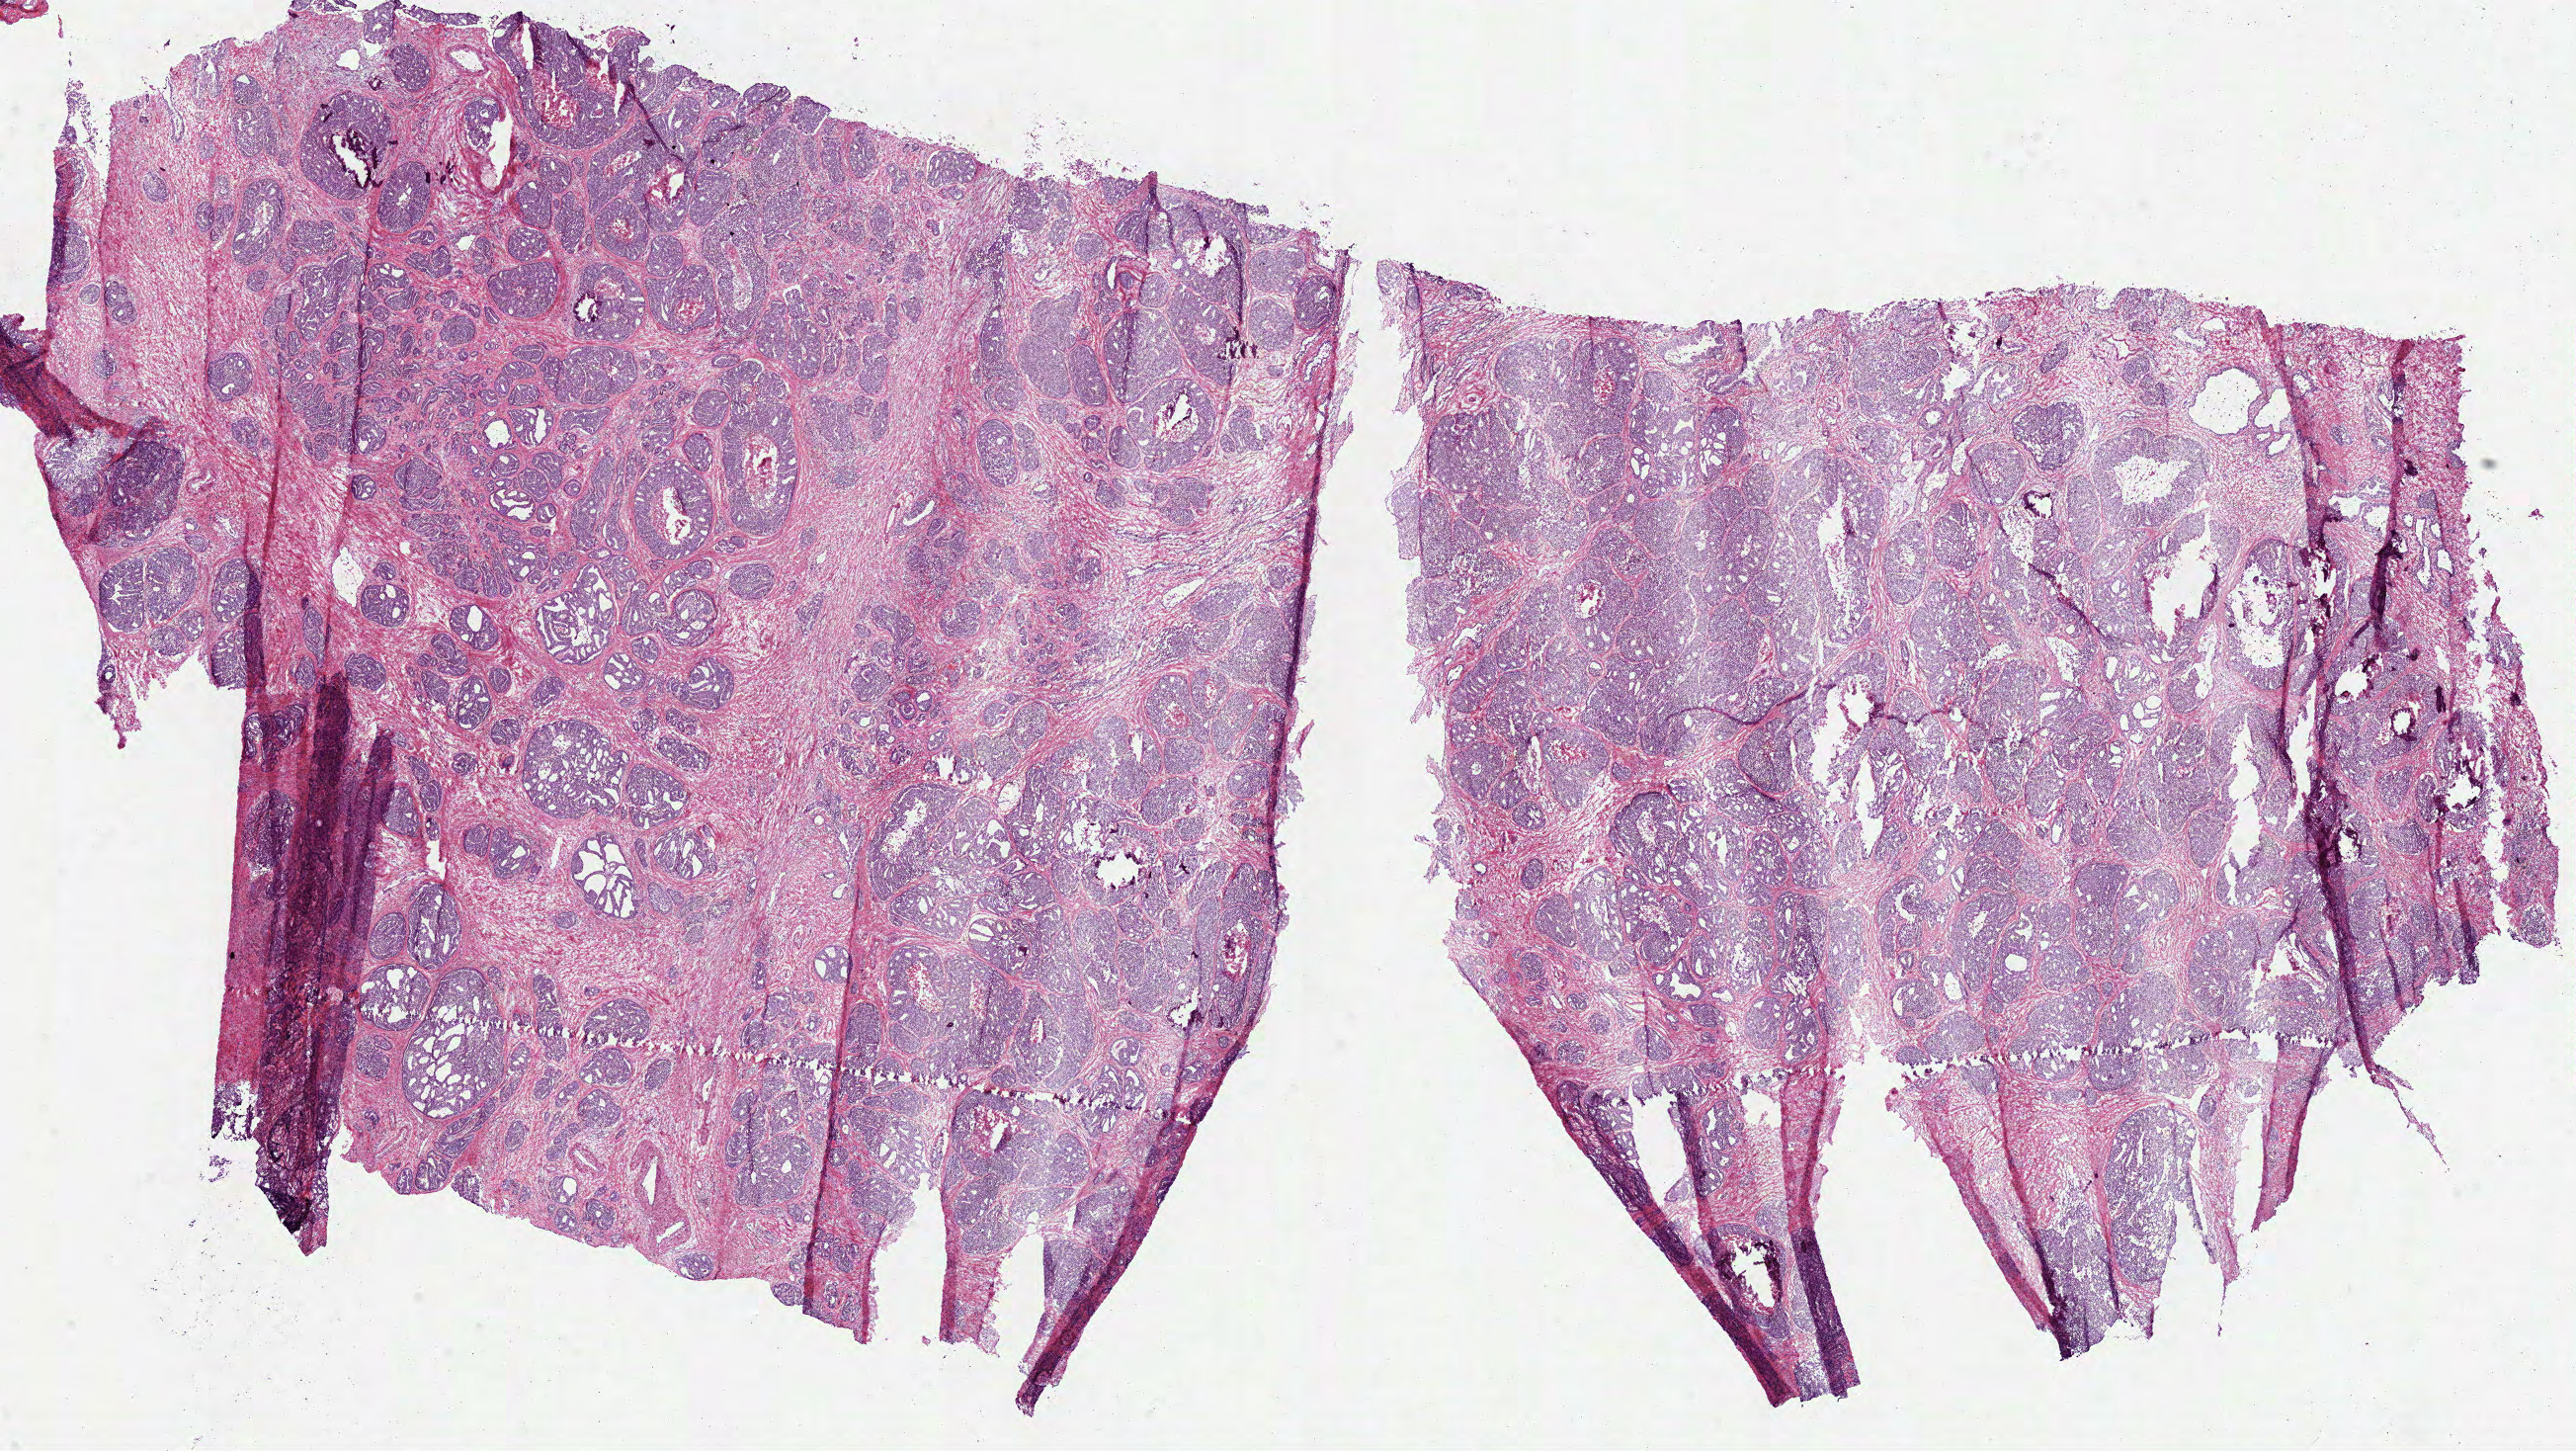
Whole-slide histology image, H&E-stained — low-resolution overview of the scanned area, about 21.0 x 11.8 mm (acquisition: 40x scan), frozen section, primary tumour sample from the prostate. Male, age 46 years at initial diagnosis. Gleason score: 9 (4+5). Slide review estimates, as recorded: tumour cells 75%, tumour nuclei 75%, normal cells 10%, stromal cells 15%, necrosis 0%.
Laterality: bilateral. Lymph nodes positive (case pathology): 0 of 57 examined. Histologic diagnosis: Acinar cell carcinoma (prostate gland).